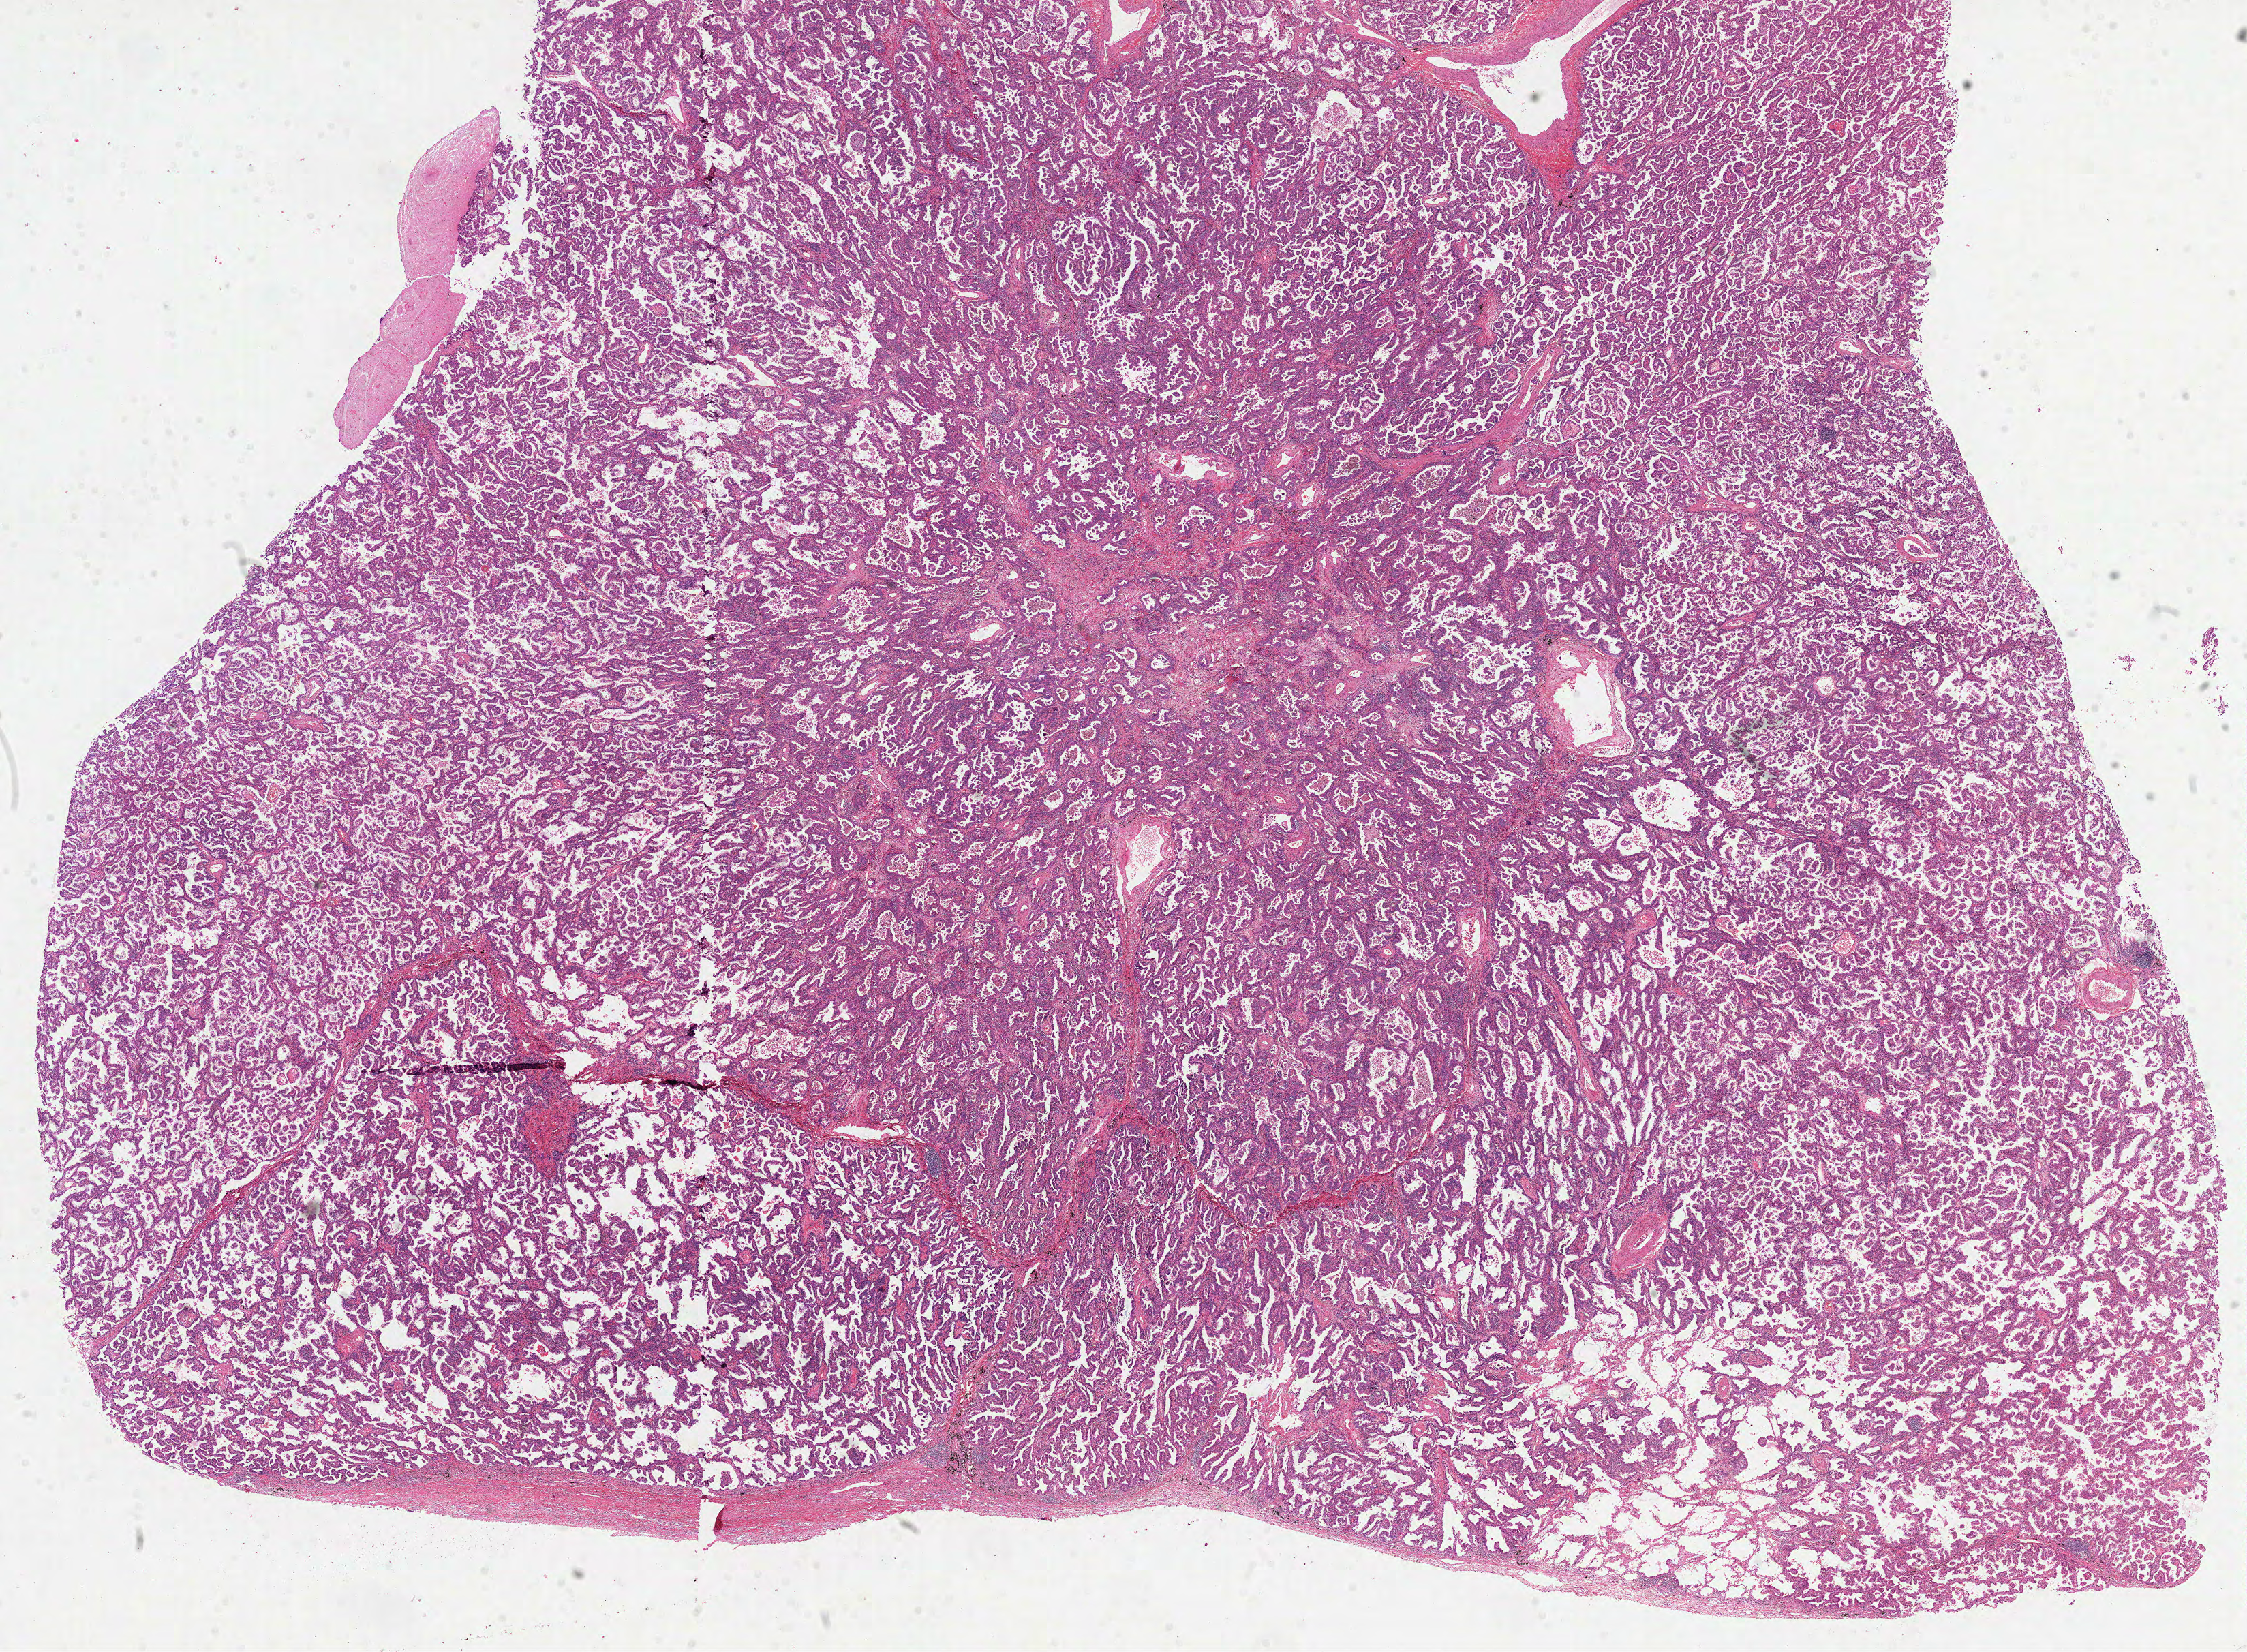
Digitized H&E-stained tissue section (whole slide), whole scanned area (about 26.6 x 19.5 mm) shown as a low-resolution overview; FFPE section; lung, primary tumour sample. Male, age 71 years at initial diagnosis.
TNM: T4 N0 M0. AJCC pathologic stage: IIIB. Pathologic diagnosis: Adenocarcinoma with mixed subtypes.